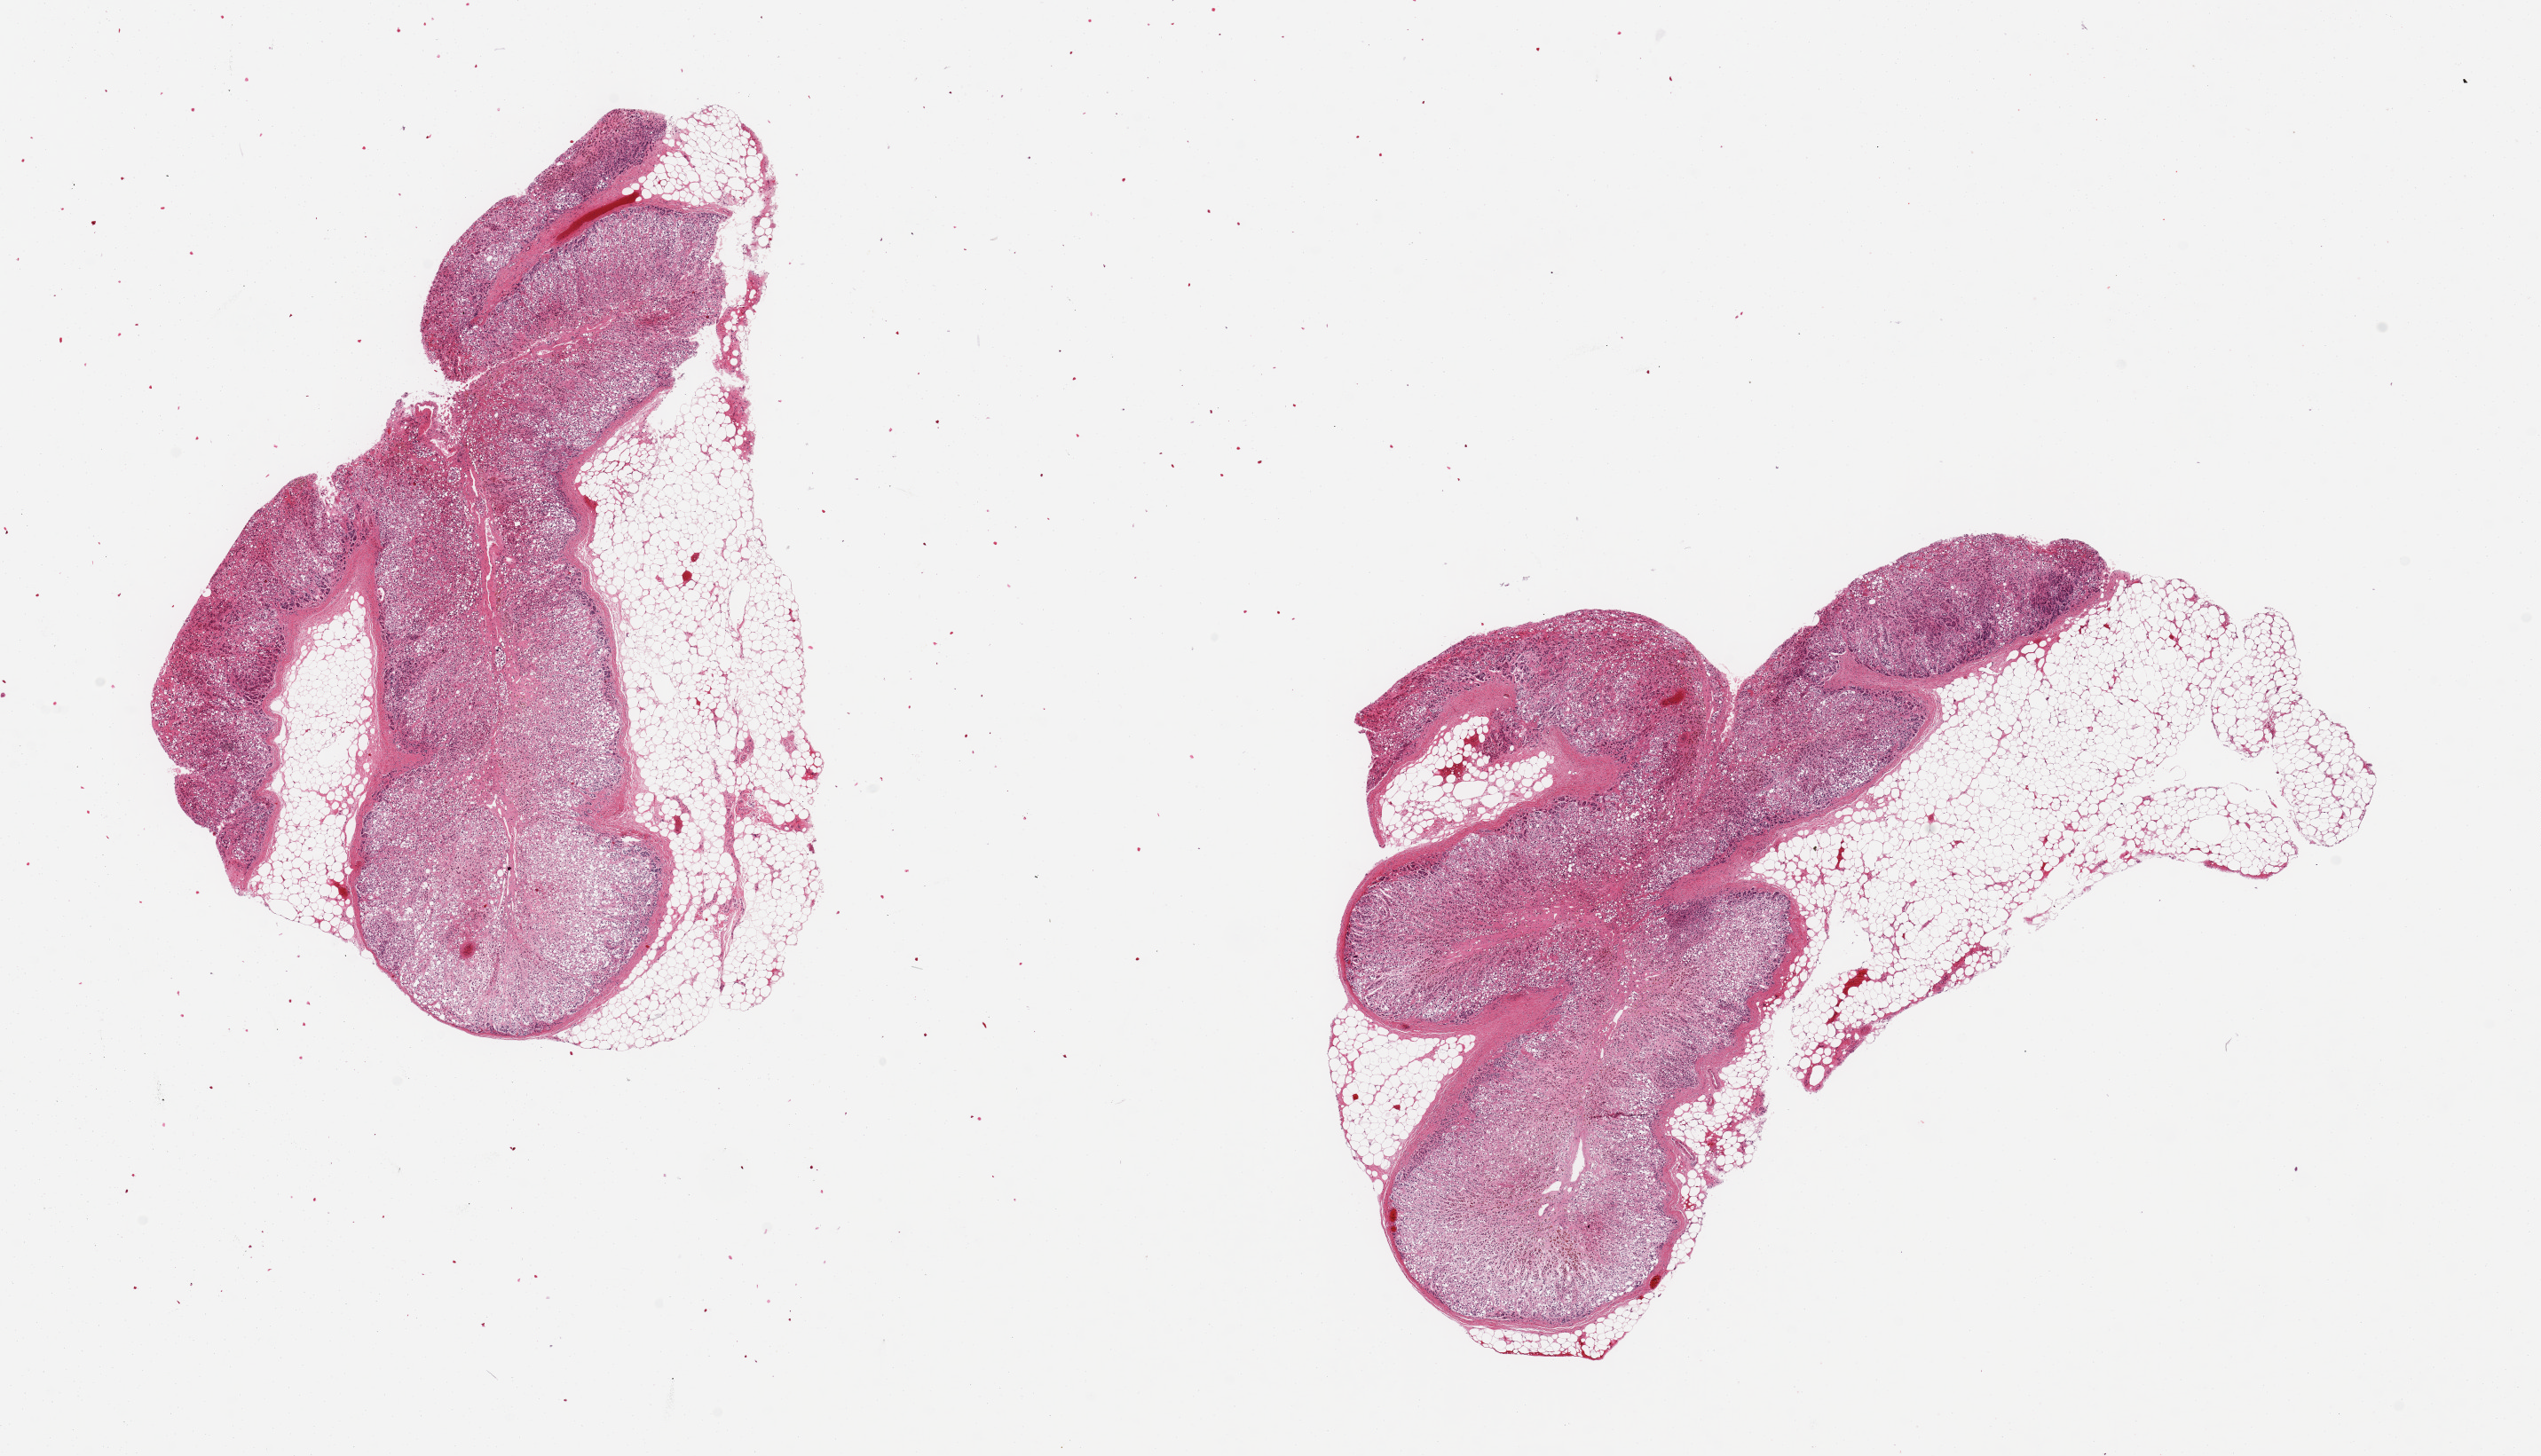
H&E whole-slide image, a low-resolution overview of the entire scanned area, about 22.6 x 13.0 mm; PAXgene-fixed paraffin-embedded (PFPE) section; sampled site (target tissue): adrenal gland; tissue donor sample. Donor sex: male.
- review note (as recorded): 2 aliquots, ~7x4mm, both ~40%% fat